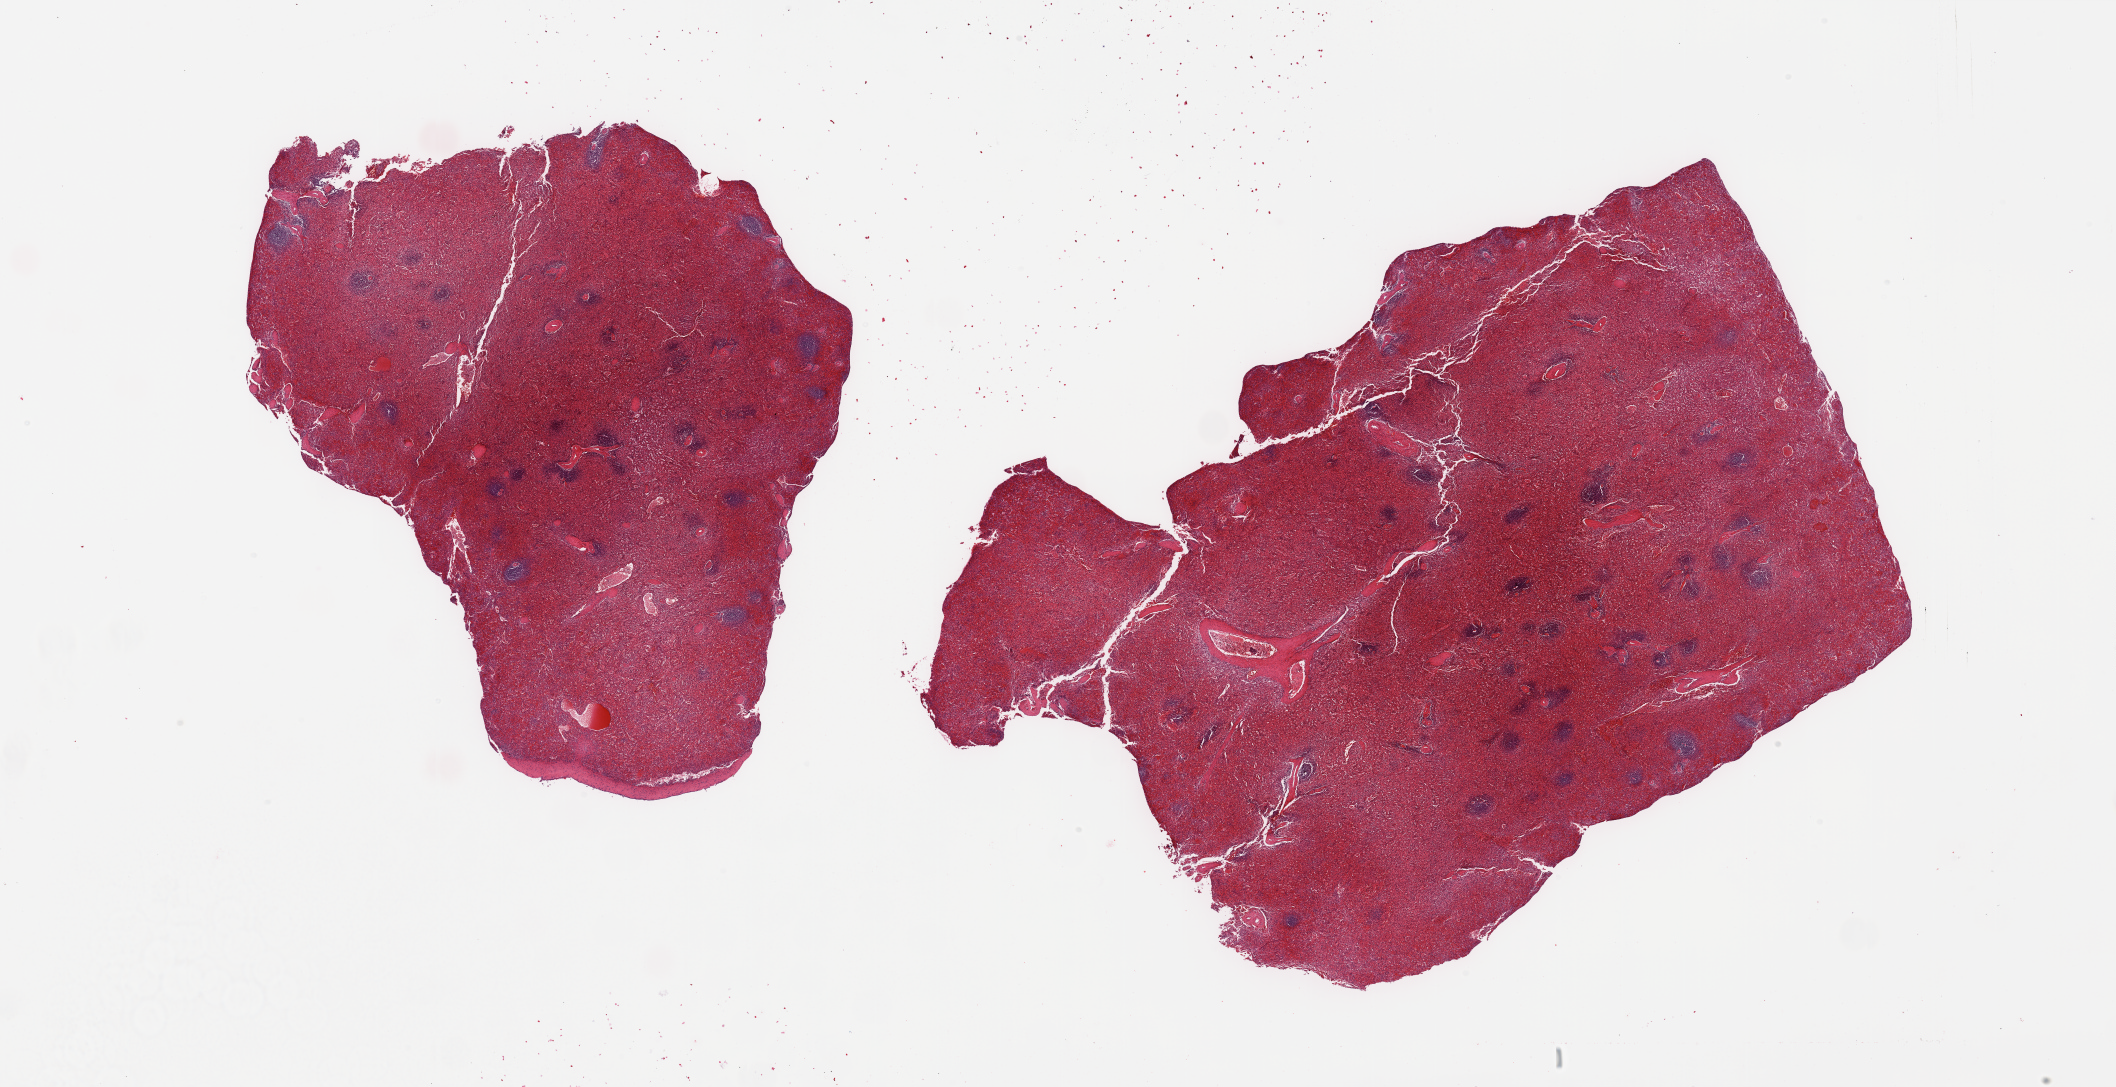
Digitized hematoxylin and eosin (H&E)-stained section, shown as a low-resolution overview of the whole scanned area (about 33.5 x 17.2 mm, acquisition: 20x scan), PAXgene-fixed, paraffin-embedded tissue, section of spleen (target tissue), donor tissue sample.
Pathologist's review note for this sample: 2 pieces; congested, portion of capsule present.